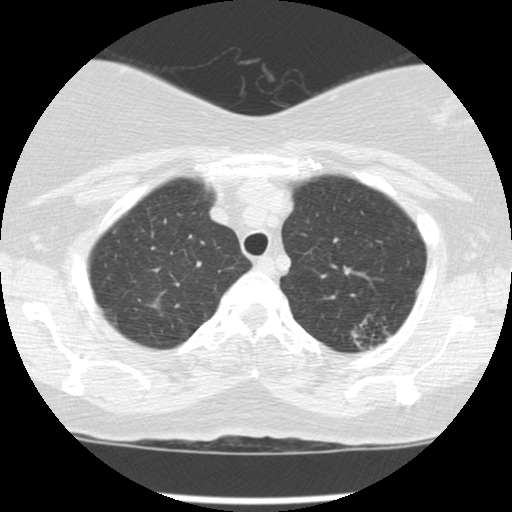
Low-dose screening chest CT, axial slice; third annual screen; lung window (W 1500 / L -600 HU); 2.5 mm slice thickness; standard (soft-tissue) reconstruction kernel (STANDARD). Female participant, aged 56 years at enrolment.
Lesion marked by an expert reader, bounding box (x1, y1, x2, y2) in pixels: (331, 300, 405, 355). The screening reader recorded 4 non-calcified nodules or masses ≥4 mm on this exam (left upper lobe, left upper lobe, left upper lobe, right upper lobe); which of them this box marks is not recorded. Later outcome: lung cancer diagnosed 49 days after this screen — adenocarcinoma, NOS, left upper lobe, moderately differentiated (G2), stage IA (AJCC 6th edition), 10 mm at pathology.